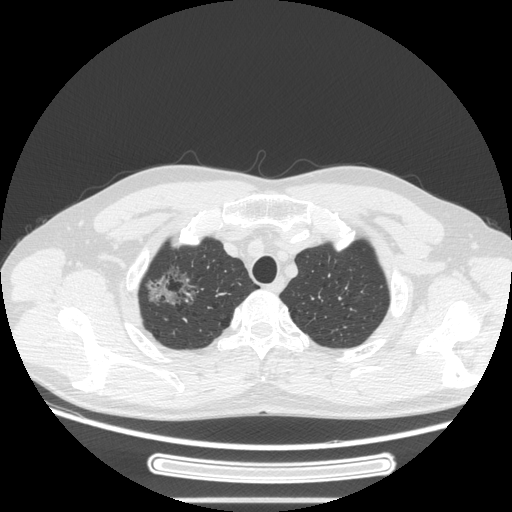
Chest CT, one axial slice; position 227 of 269 along the scan axis; 120 kVp; lung window (W 1500 / L -600 HU); 1.25 mm slice thickness; 512 × 512 image matrix. Male patient, age 53 years. Case-level facts recorded for this patient, not image findings: clinical TNM (as recorded): T1c N0 M0; histopathological grade: G2.
Outlined on this slice (bounding box drawn by a radiologist):
- lung tumour (recorded histology: adenocarcinoma): box from (x=141, y=261) to (x=201, y=321) px